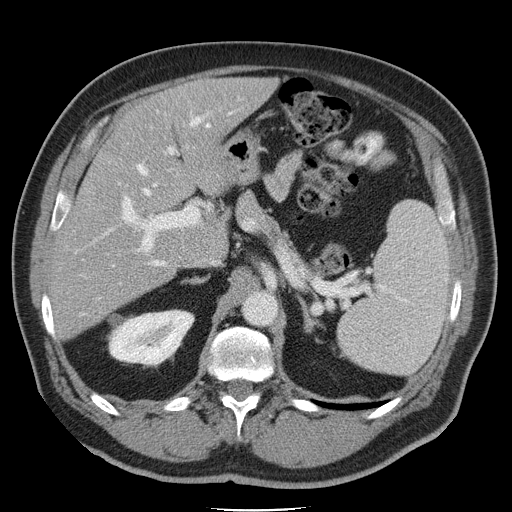
Contrast-enhanced abdominal CT, one axial slice. Slice 27 of 45 in the series (ordered by position). 120 kVp. Intravenous contrast given. Soft-tissue window (W 400 / L 40 HU). 5 mm slice thickness. 512 × 512 image matrix, field of view 386 × 386 mm. Male patient, age 65 years. From the clinical record (not read from this slice): diagnosis: colorectal cancer liver metastases, imaged before liver resection; multiple liver metastases: yes; largest metastasis: 4.9 cm; disease in both lobes: no.
Annotated regions visible in this slice (expert manual segmentation):
- hepatic veins: bounding box [x1, y1, x2, y2] px = [136, 111, 235, 266]
- liver: [53, 79, 271, 334]
- planned liver remnant (the part of the liver to remain after resection): [105, 79, 271, 248]
- portal vein (with intrahepatic branches): [91, 113, 212, 264]